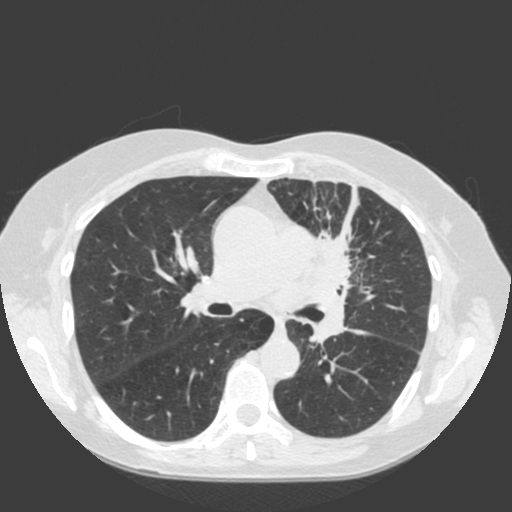
Low-dose screening chest CT, one axial slice. Slice 113 of 184 in the series (ordered by position). 120 kVp. Lung window (W 1500 / L -600 HU). 2 mm slice thickness. 512 × 512 image matrix, field of view 350 × 350 mm.
Structures marked on this image (manually delineated by an expert):
- lesion 1 (tumor, hilum of left lung): bounding box [x1, y1, x2, y2] px = [306, 229, 352, 344]